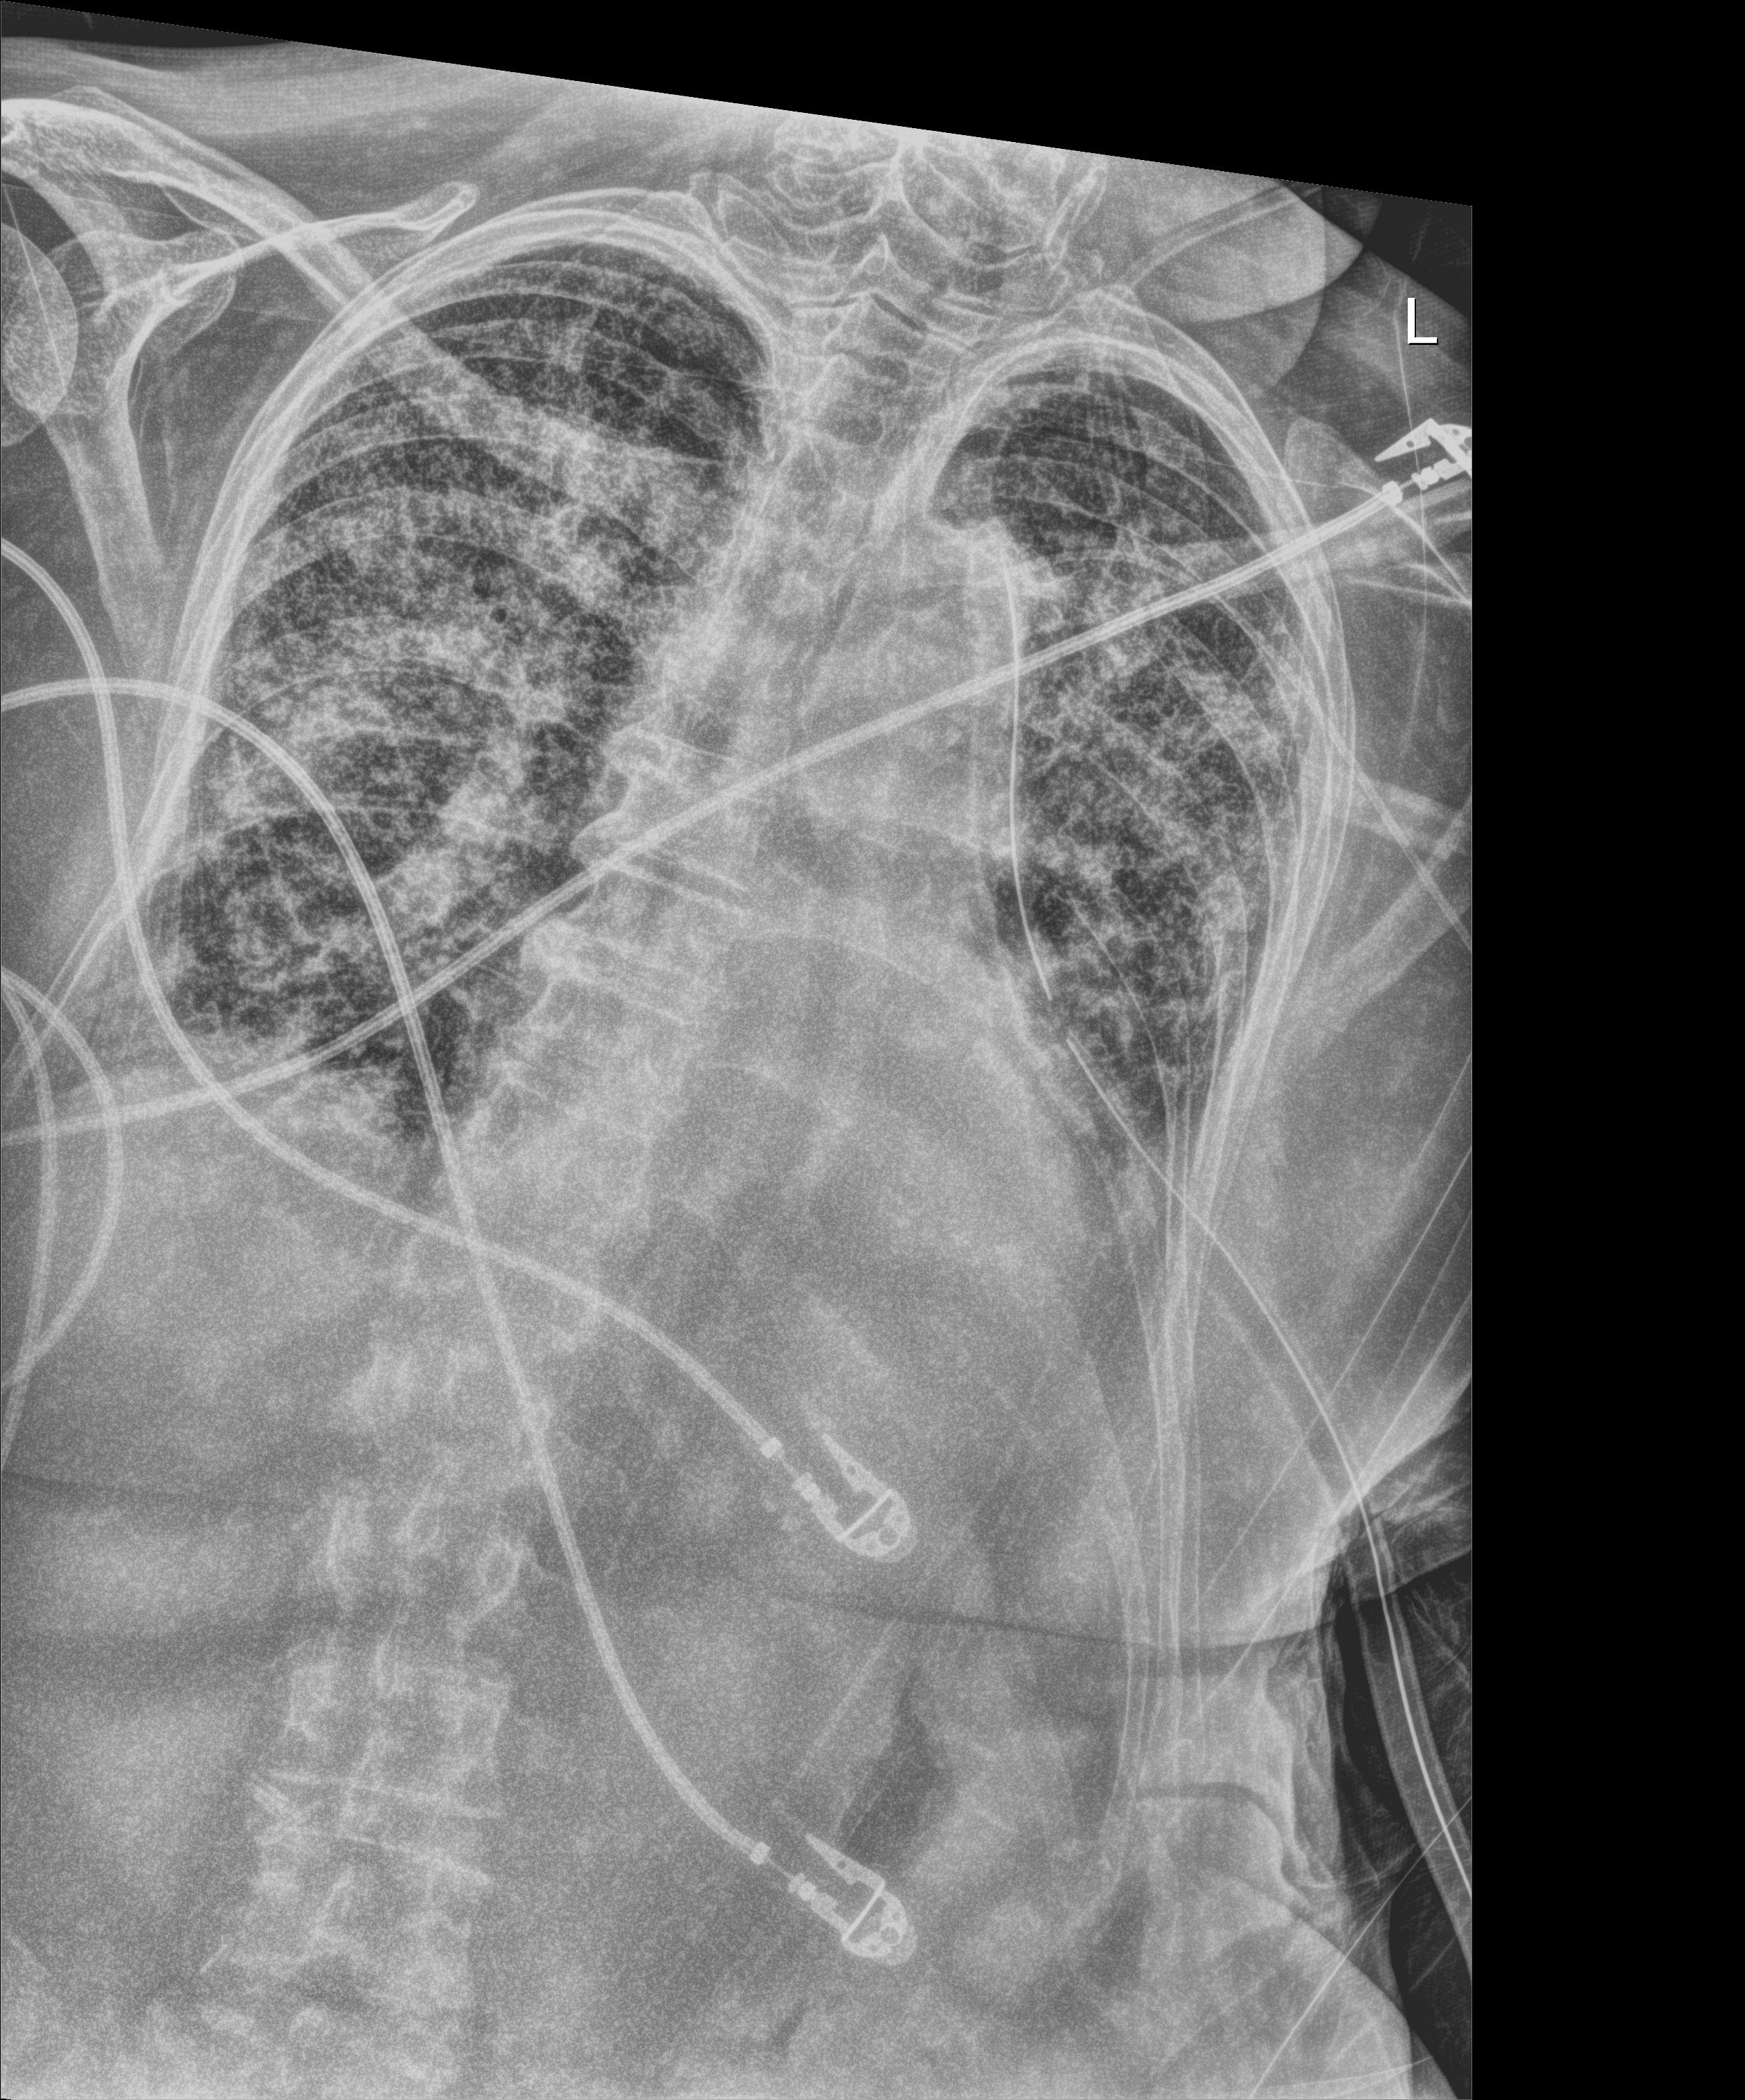
Bedside chest radiograph (digital radiography); anteroposterior (AP) projection. Patient hospitalised with COVID-19; female, aged 75–90 years.
From the hospital-stay record, not from the radiograph (when in the stay this image was taken is not recorded): mechanically ventilated during this hospital stay: yes.